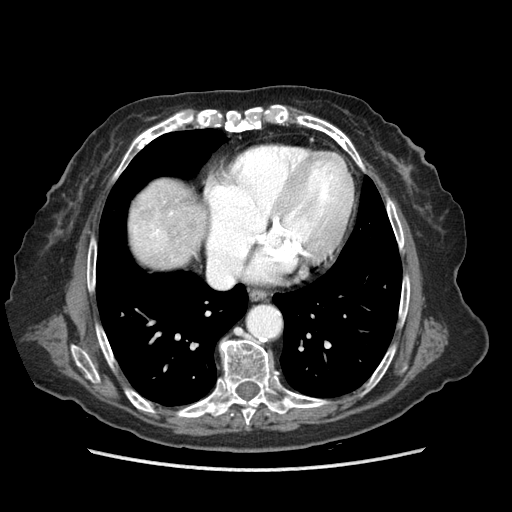
Contrast-enhanced abdominal CT (liver protocol), one axial slice. Slice 80 of 89 in the series (ordered by position). 140 kVp. Soft-tissue window (W 400 / L 40 HU). 512 × 512 image matrix. From the clinical record (not read from this slice): diagnosis: hepatocellular carcinoma (patient treated with transarterial chemoembolisation; whether this scan precedes or follows treatment is not stated here); TNM stage (as recorded): Stage-IIIA; Child-Pugh class: A; tumour differentiation: well differentiated; tumour size: 11 cm.
Outlined on this slice (semi-automatically segmented with operator editing):
- liver parenchyma outside the tumour (the mass and vessels are separate outlines, so this box may not span the whole liver): box from (x=129, y=178) to (x=206, y=268) px
- liver vessels: (x=135, y=212)–(x=172, y=239)